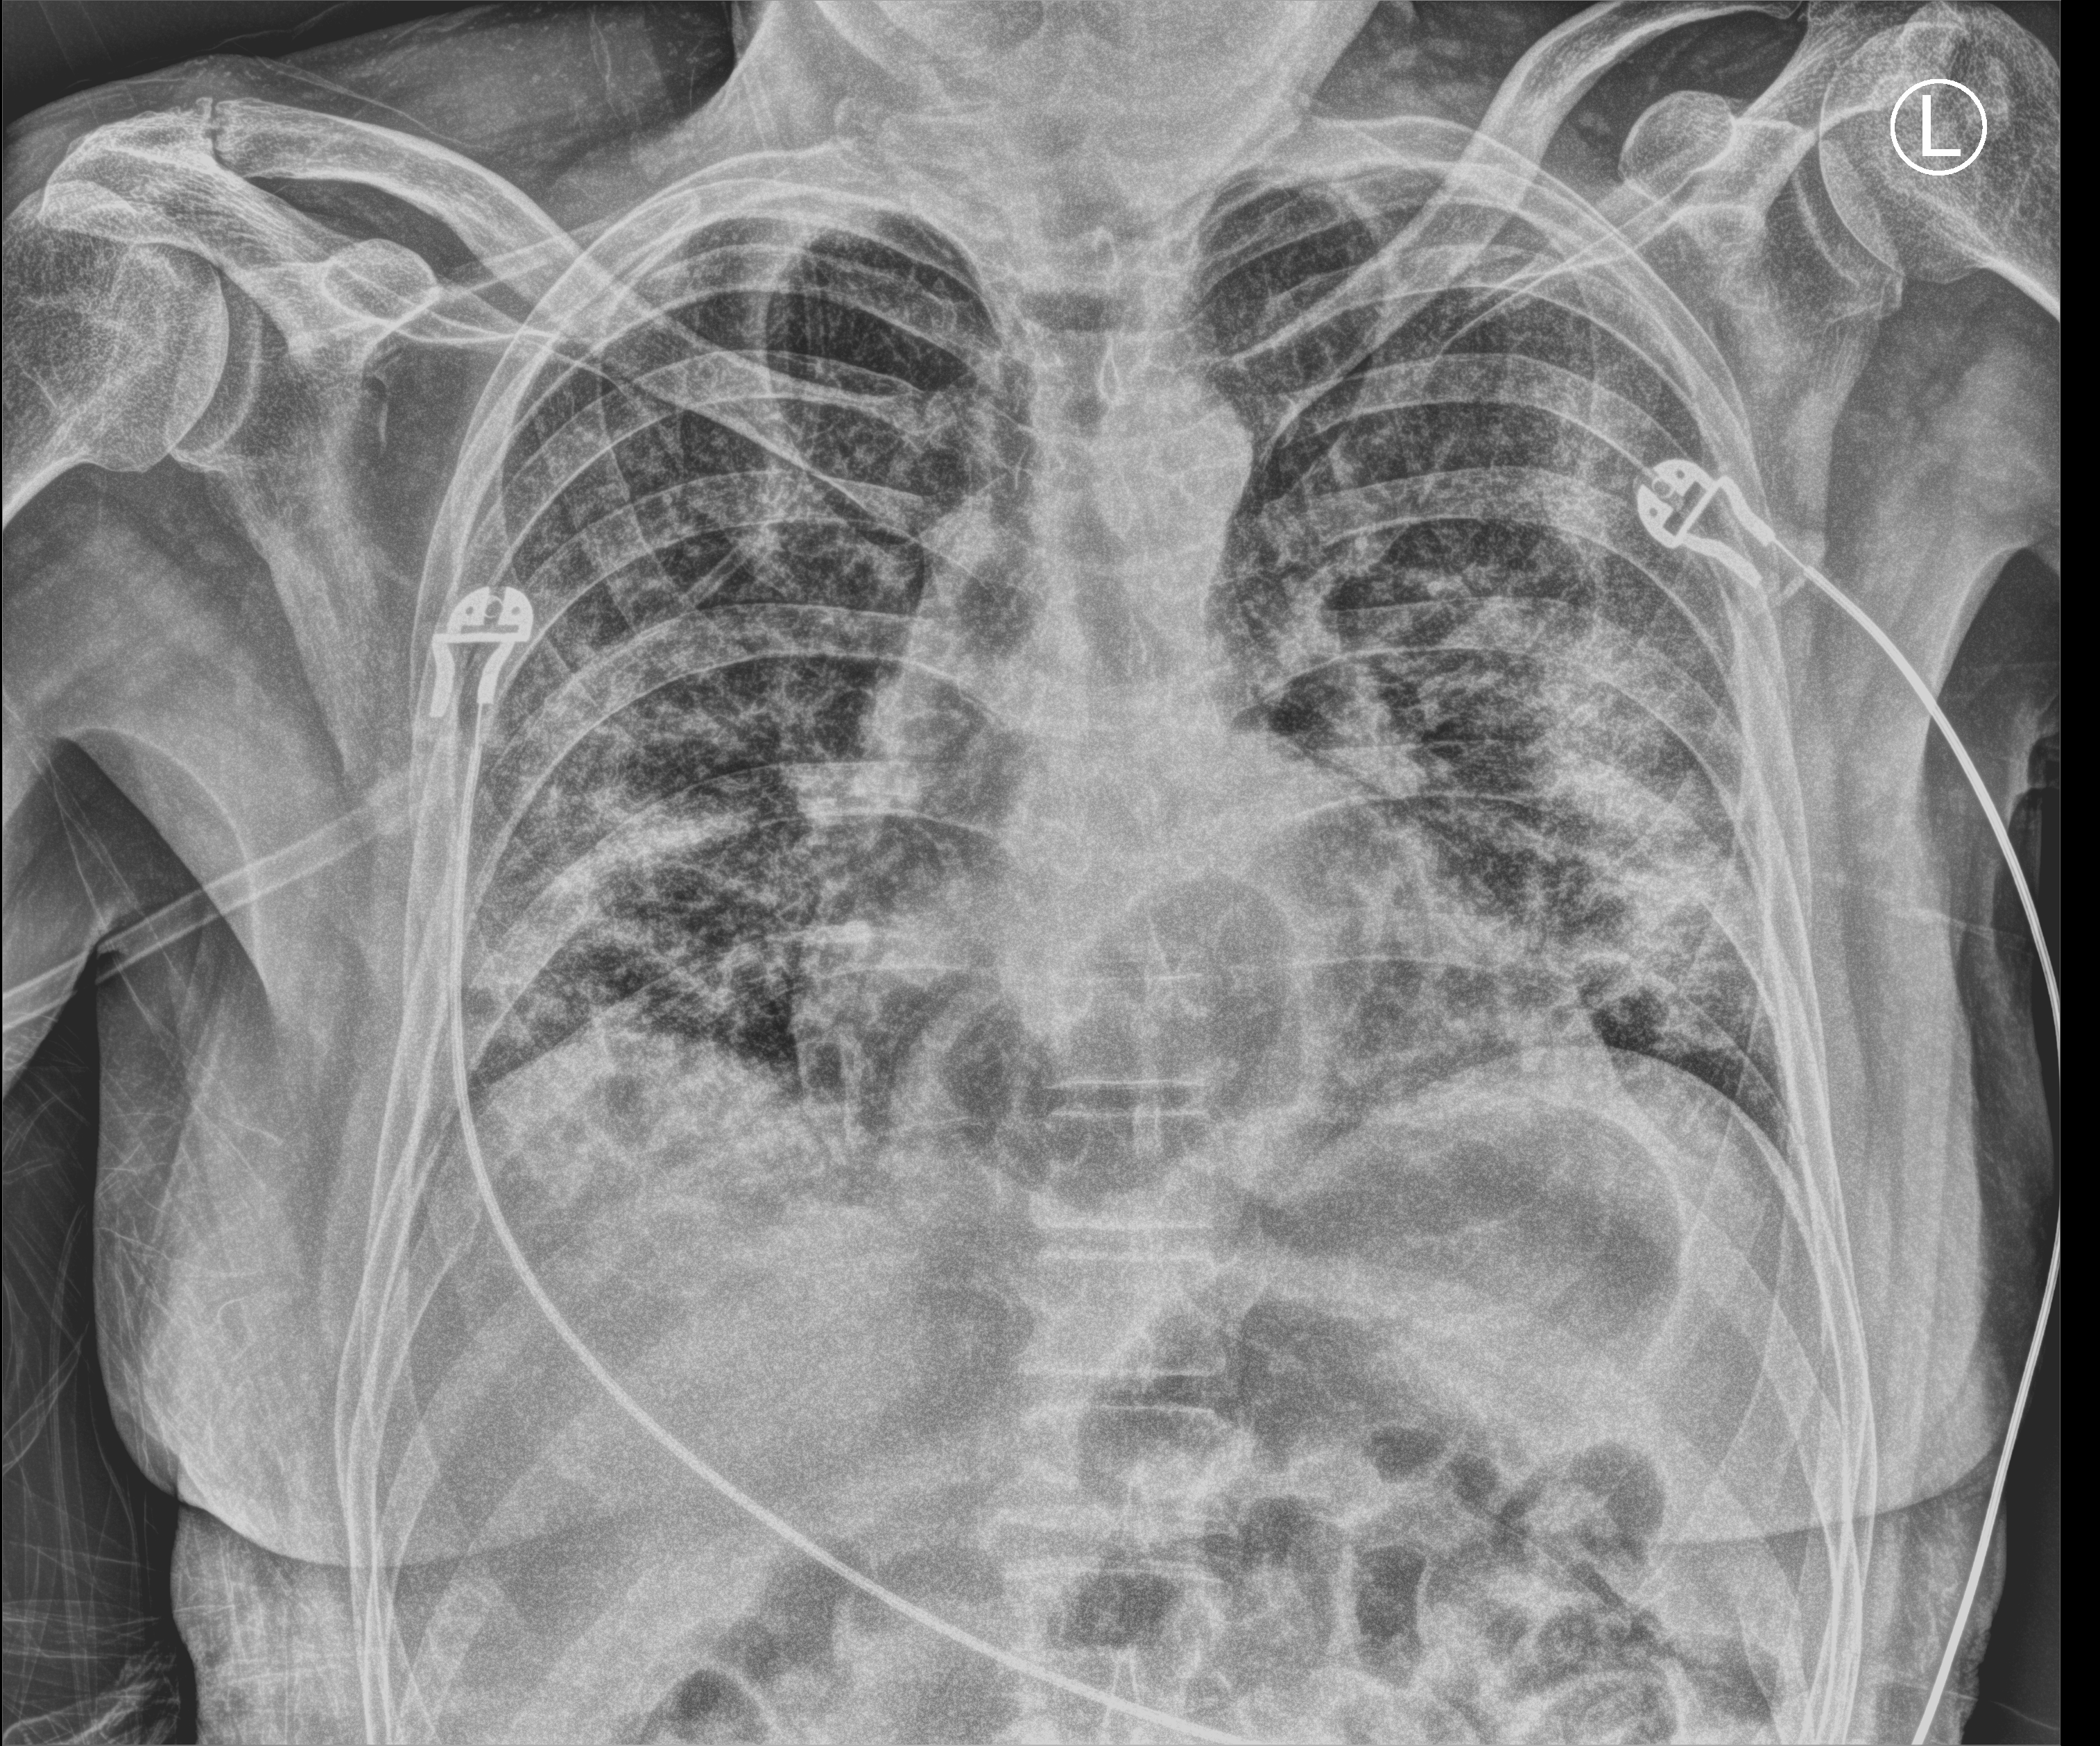
Portable chest radiograph; anteroposterior (AP) projection. Male patient hospitalised with COVID-19, age 60–74 years.
Admission-level facts for this patient (not findings on this image; timing relative to this image not recorded): admitted to intensive care during this hospital stay: no.